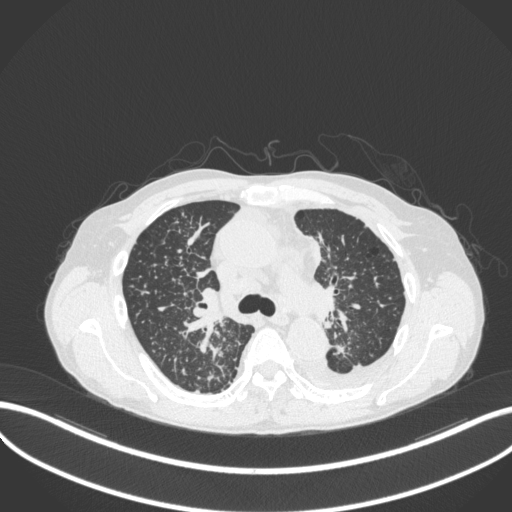
Chest CT, one axial slice; position 241 of 319 along the scan axis; reconstruction kernel B31f; lung window (W 1500 / L -600 HU); 512 × 512 image matrix. Male patient, age 58 years. Case-level facts recorded for this patient, not image findings: clinical TNM (as recorded): T1c N3 M1.
Structures marked on this image (bounding box drawn by a radiologist):
- lung tumour (recorded histology: adenocarcinoma): box from (x=330, y=340) to (x=351, y=362) px